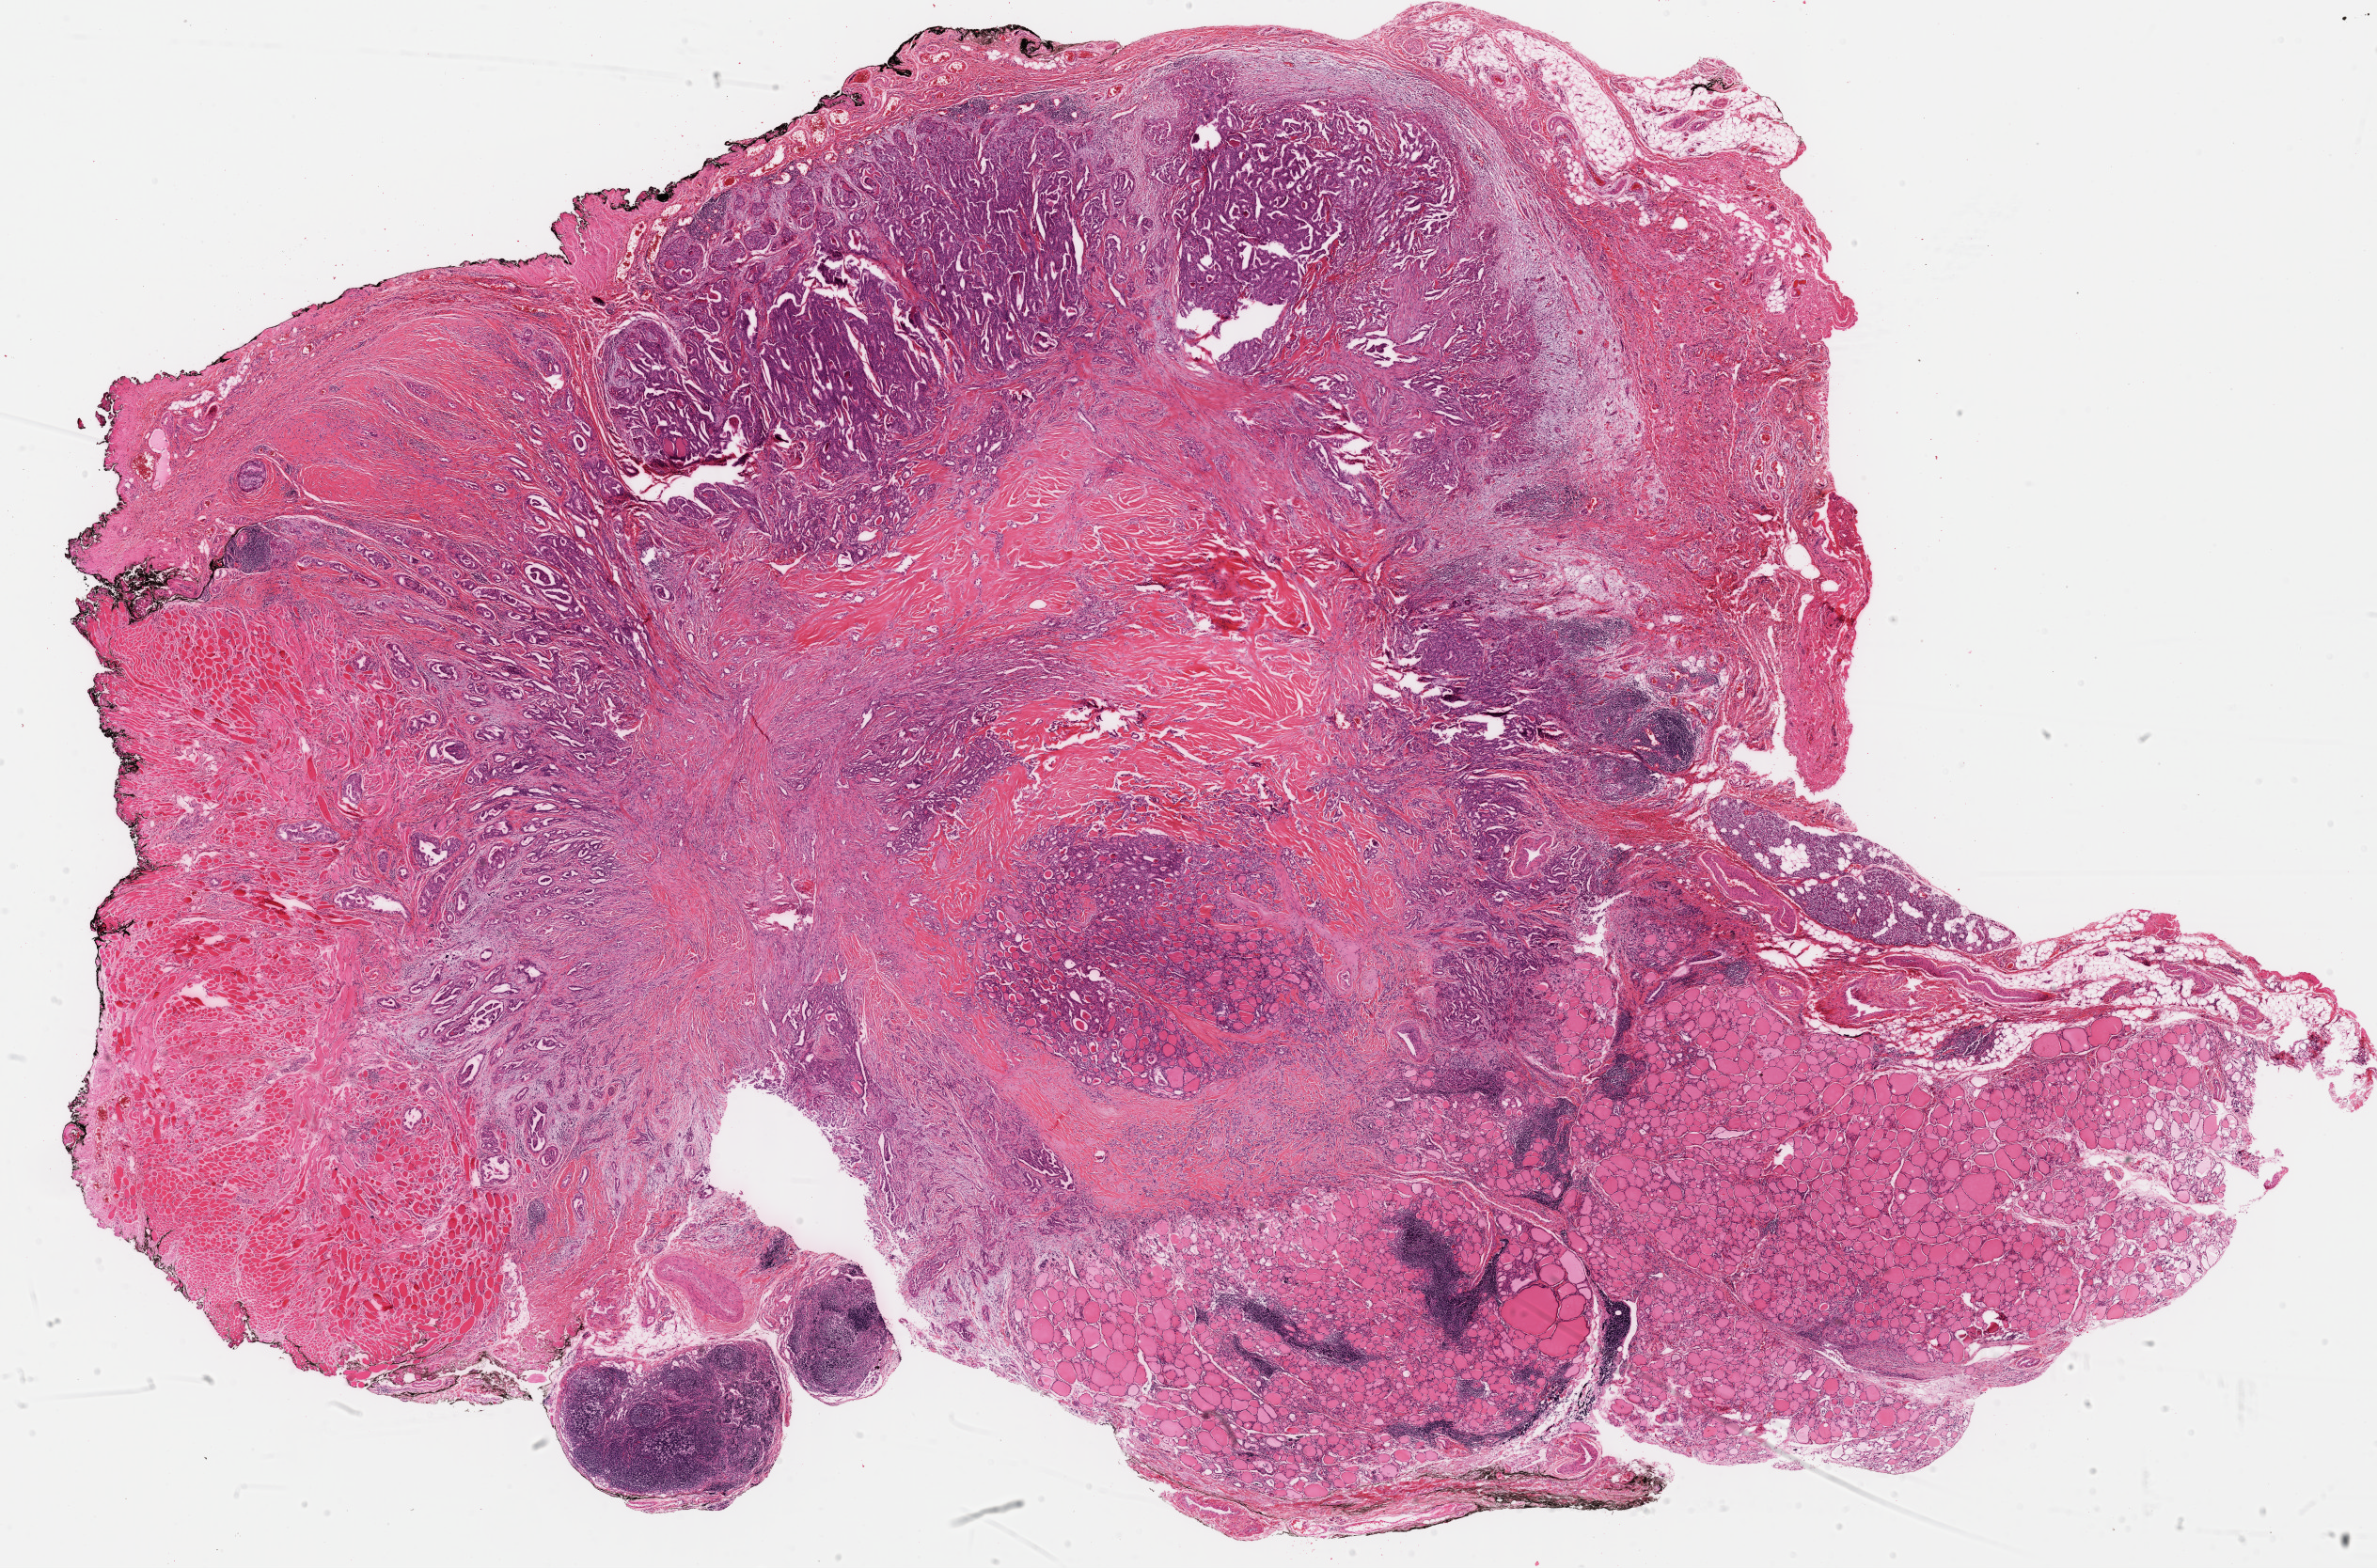
Hematoxylin and eosin (H&E) stained whole-slide image — shown as a low-resolution overview of the whole scanned area (about 20.0 x 13.2 mm), formalin-fixed paraffin-embedded (FFPE) diagnostic section, primary tumour sample from the thyroid. Female patient; age at initial diagnosis 70 years.
Histologic diagnosis: Papillary adenocarcinoma, NOS (thyroid gland). AJCC pathologic stage: III.